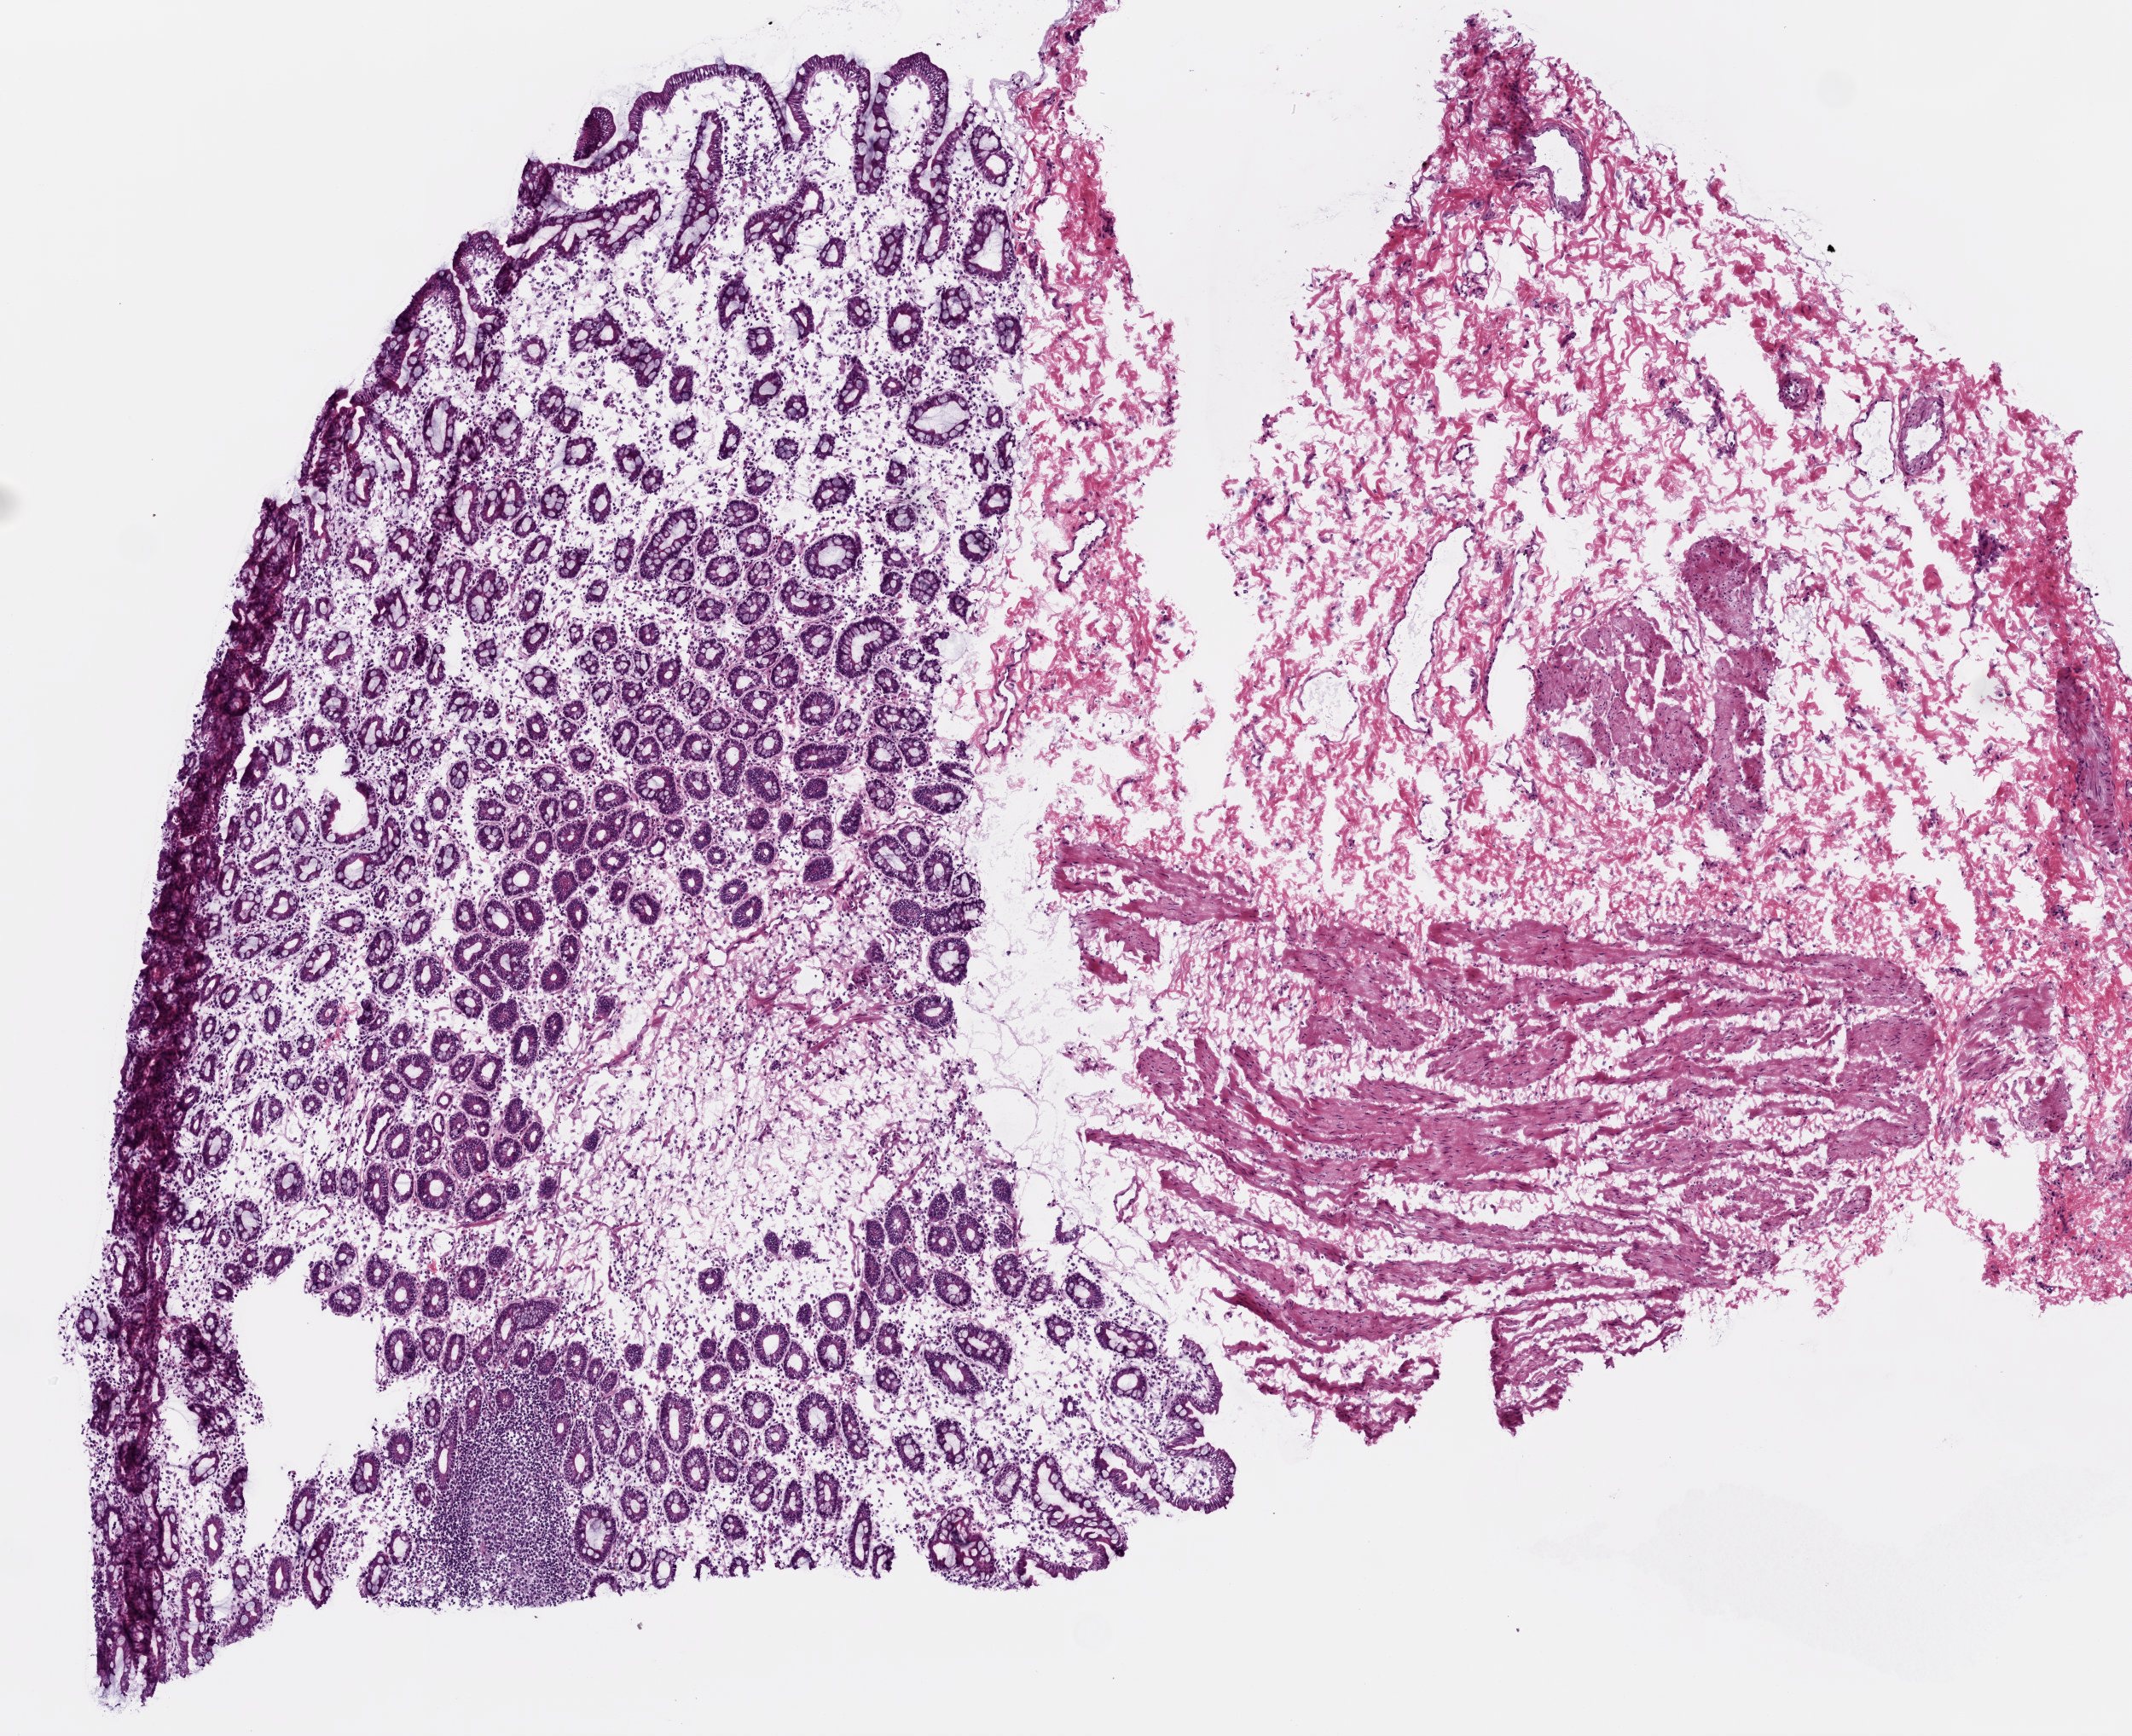
Whole-slide histology image, H&E — a low-resolution overview of the entire scanned area, about 5.0 x 4.1 mm; frozen section from the top of the tissue portion; solid tissue normal (non-tumour tissue) sample from the stomach. Patient: female, age at initial diagnosis 80 years.
• this section: solid tissue normal sample (biorepository sample class)
• patient diagnosis: Adenocarcinoma, intestinal type